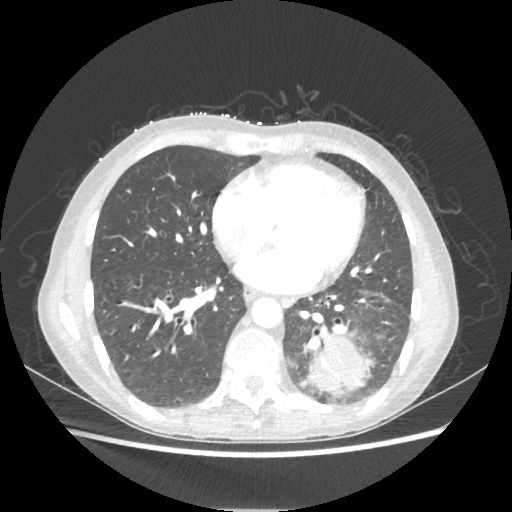
Chest CT, one axial slice. 80 kVp. Lung window (W 1500 / L -600 HU). 1.25 mm slice thickness. 512 × 512 image matrix. Female patient, age 53 years. From the clinical record (not read from this slice): clinical TNM (as recorded): T3 N0 M0.
Outlined on this slice (rectangle marked by the reading radiologist):
- lung tumour (recorded histology: adenocarcinoma): box from (x=304, y=331) to (x=372, y=398) px